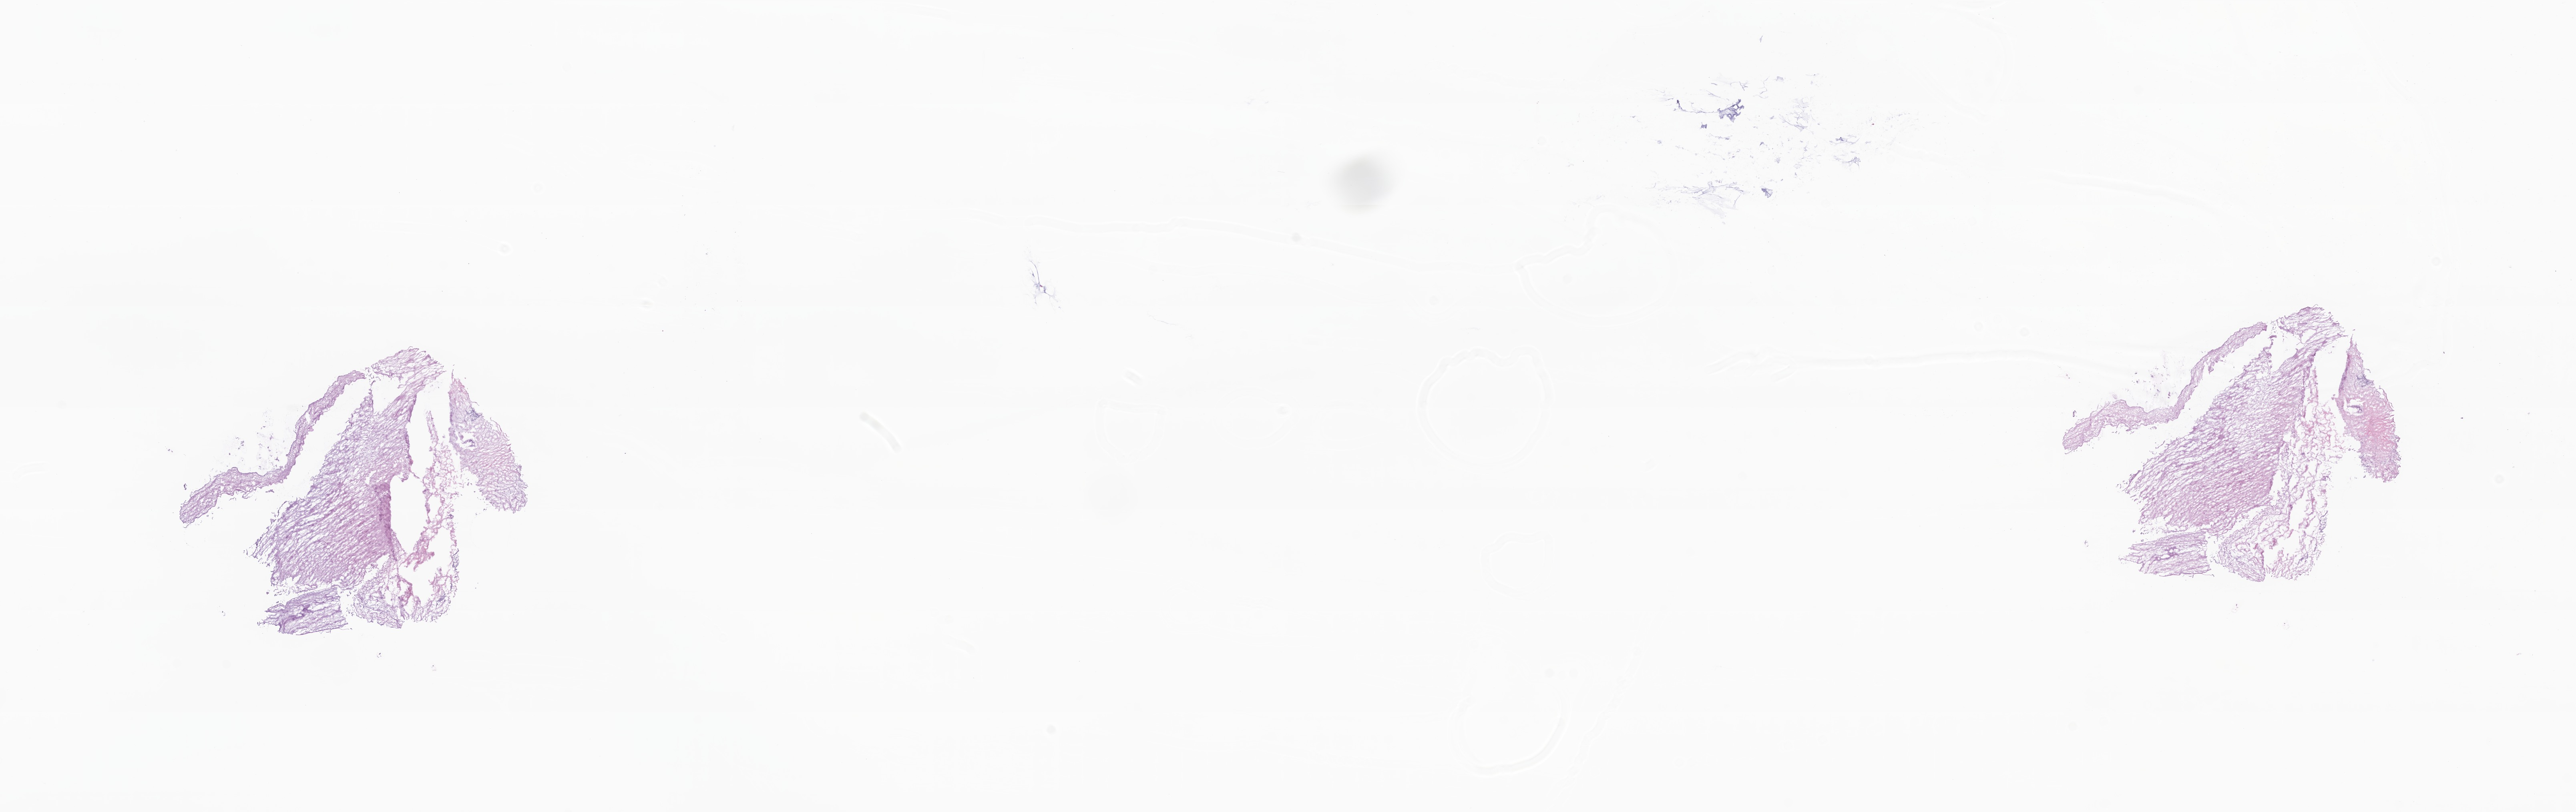
Haematoxylin and eosin whole-slide image — low-resolution overview of the scanned area, about 27.1 x 8.6 mm; frozen section (tissue freezing medium); specimen: primary tumor; site: body of pancreas. Male, age 74 years at initial diagnosis. Slide review estimates, as recorded: tumor cells 1%, tumor nuclei 70%, stromal cells 99%, necrosis 0%, normal cells 0%. Infiltration values recorded for this section: lymphocyte infiltration 4%, monocyte infiltration 0%, neutrophil infiltration 0%.
• diagnosis: Infiltrating duct carcinoma, NOS